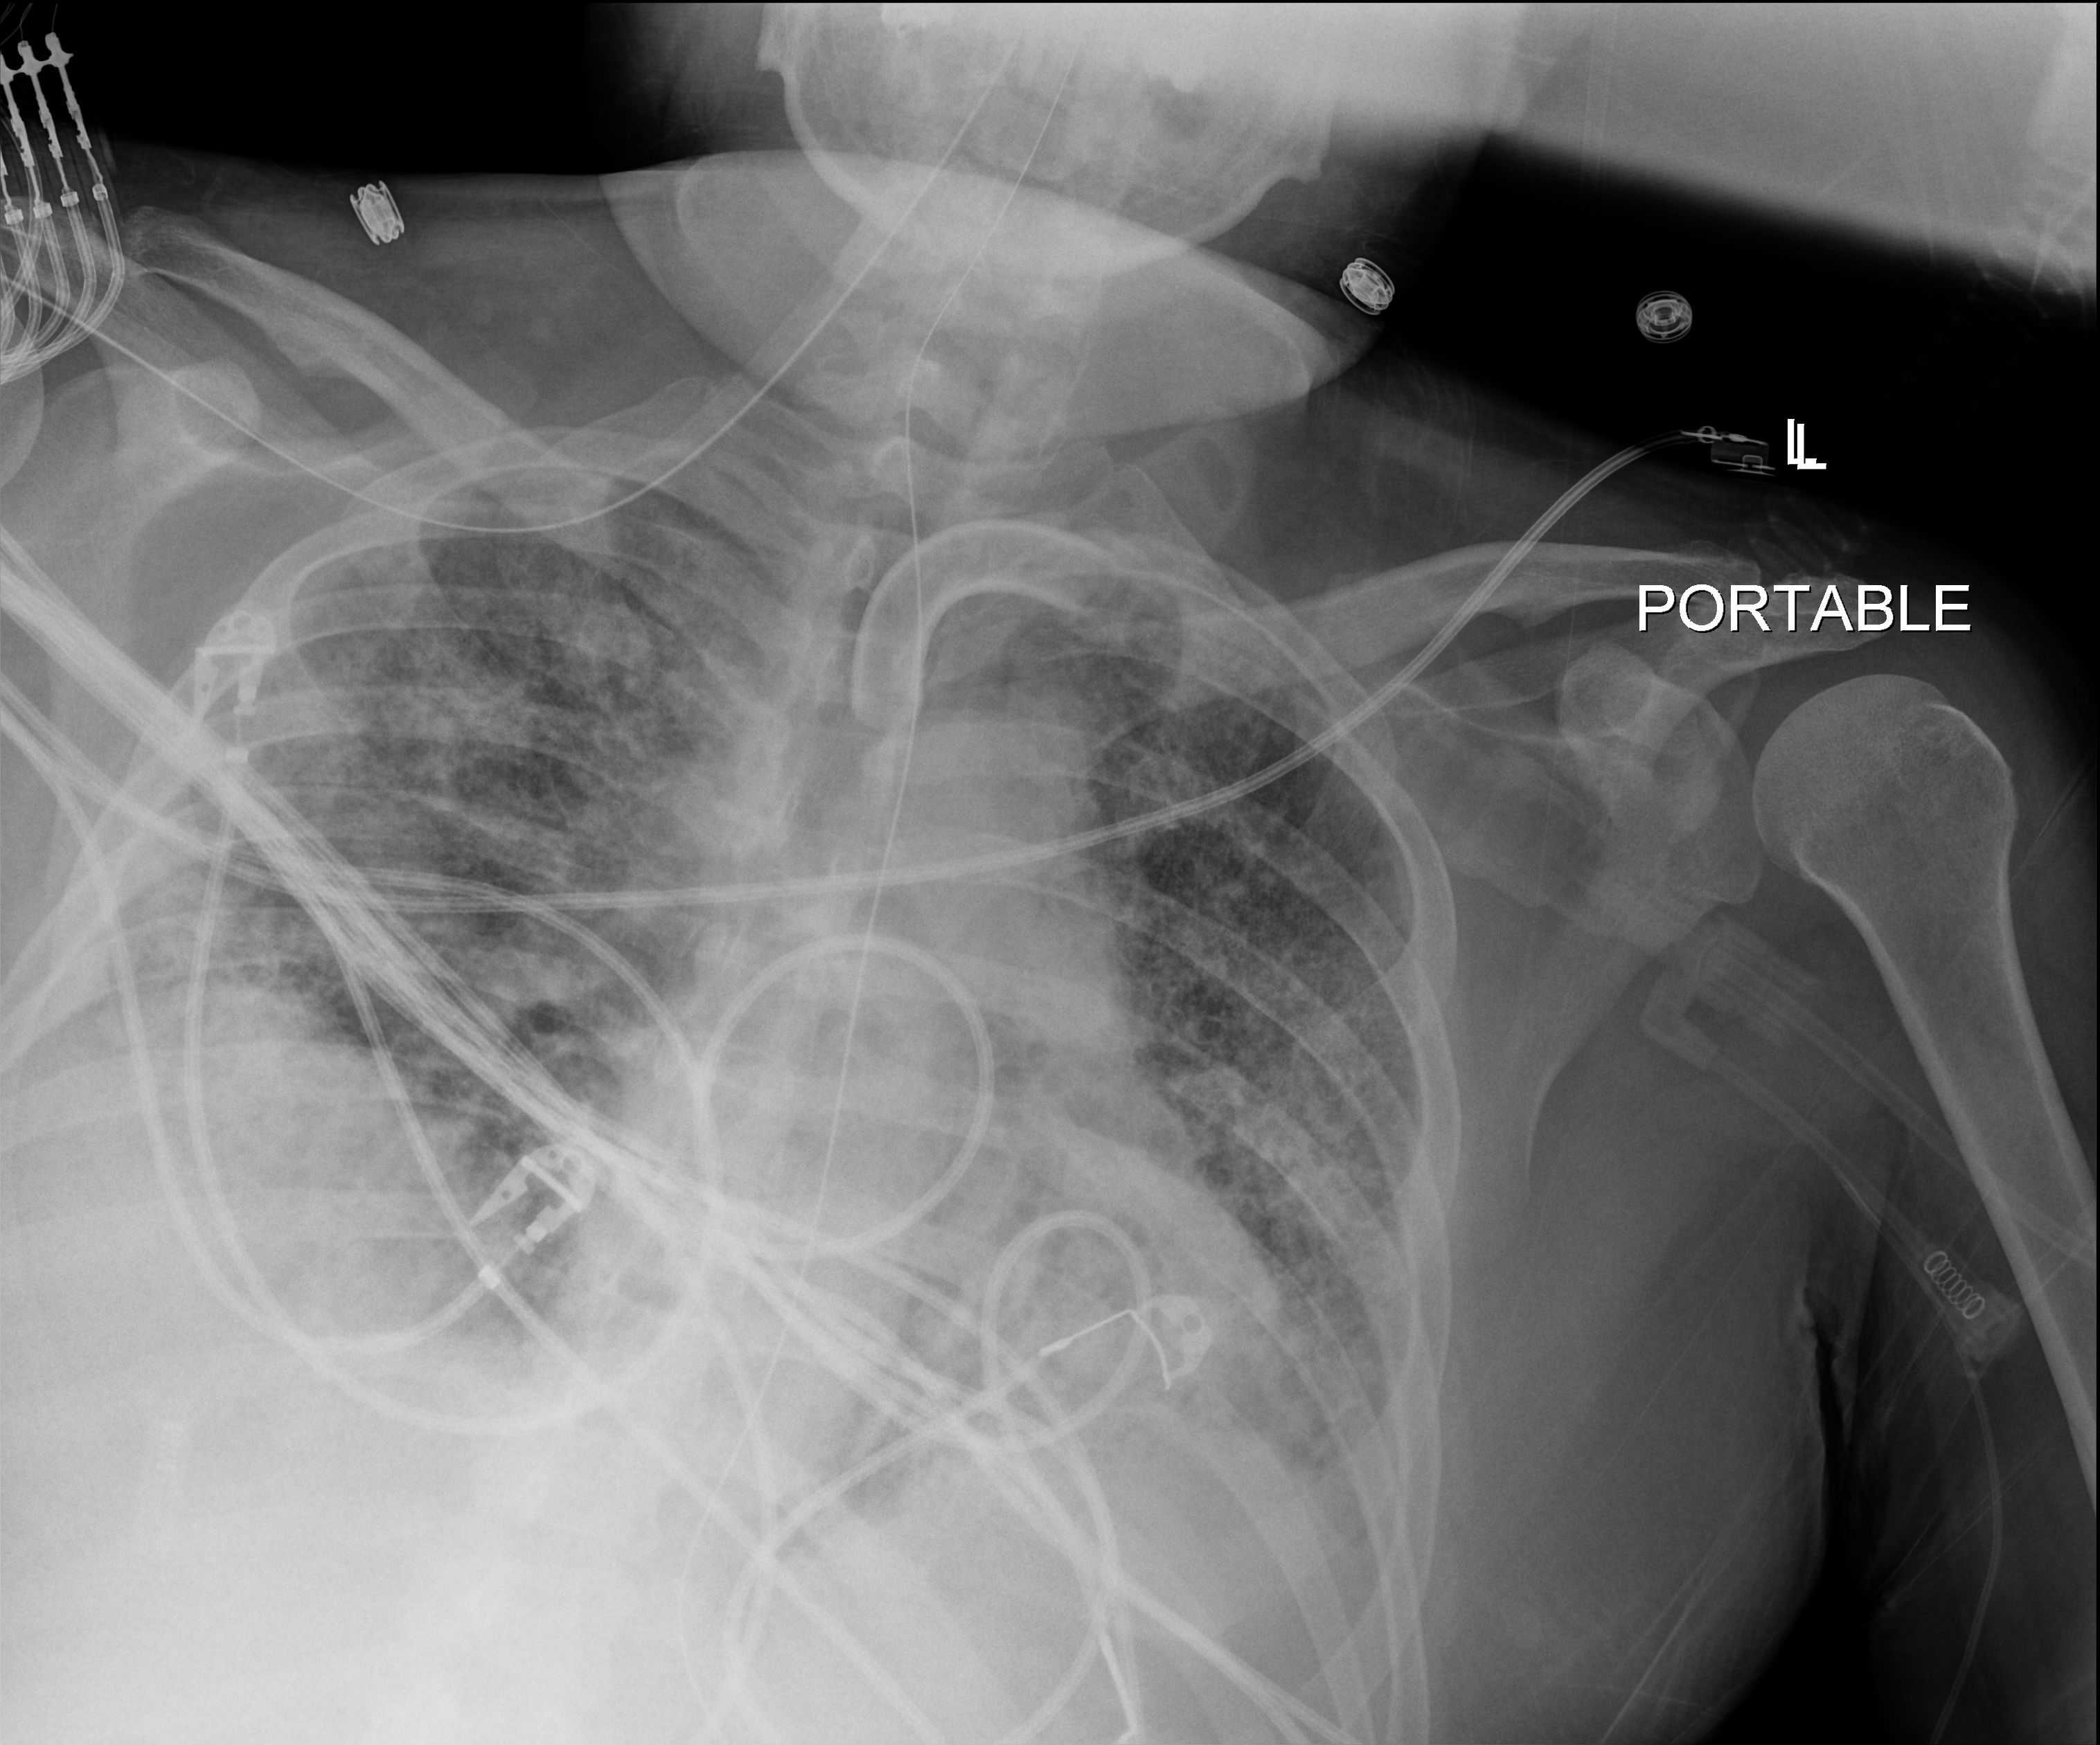
Portable chest radiograph, anteroposterior (AP) projection. Patient hospitalised with COVID-19; male, aged 18–59 years.
From the hospital-stay record, not from the radiograph (when in the stay this image was taken is not recorded): smoking status (admission record): never.